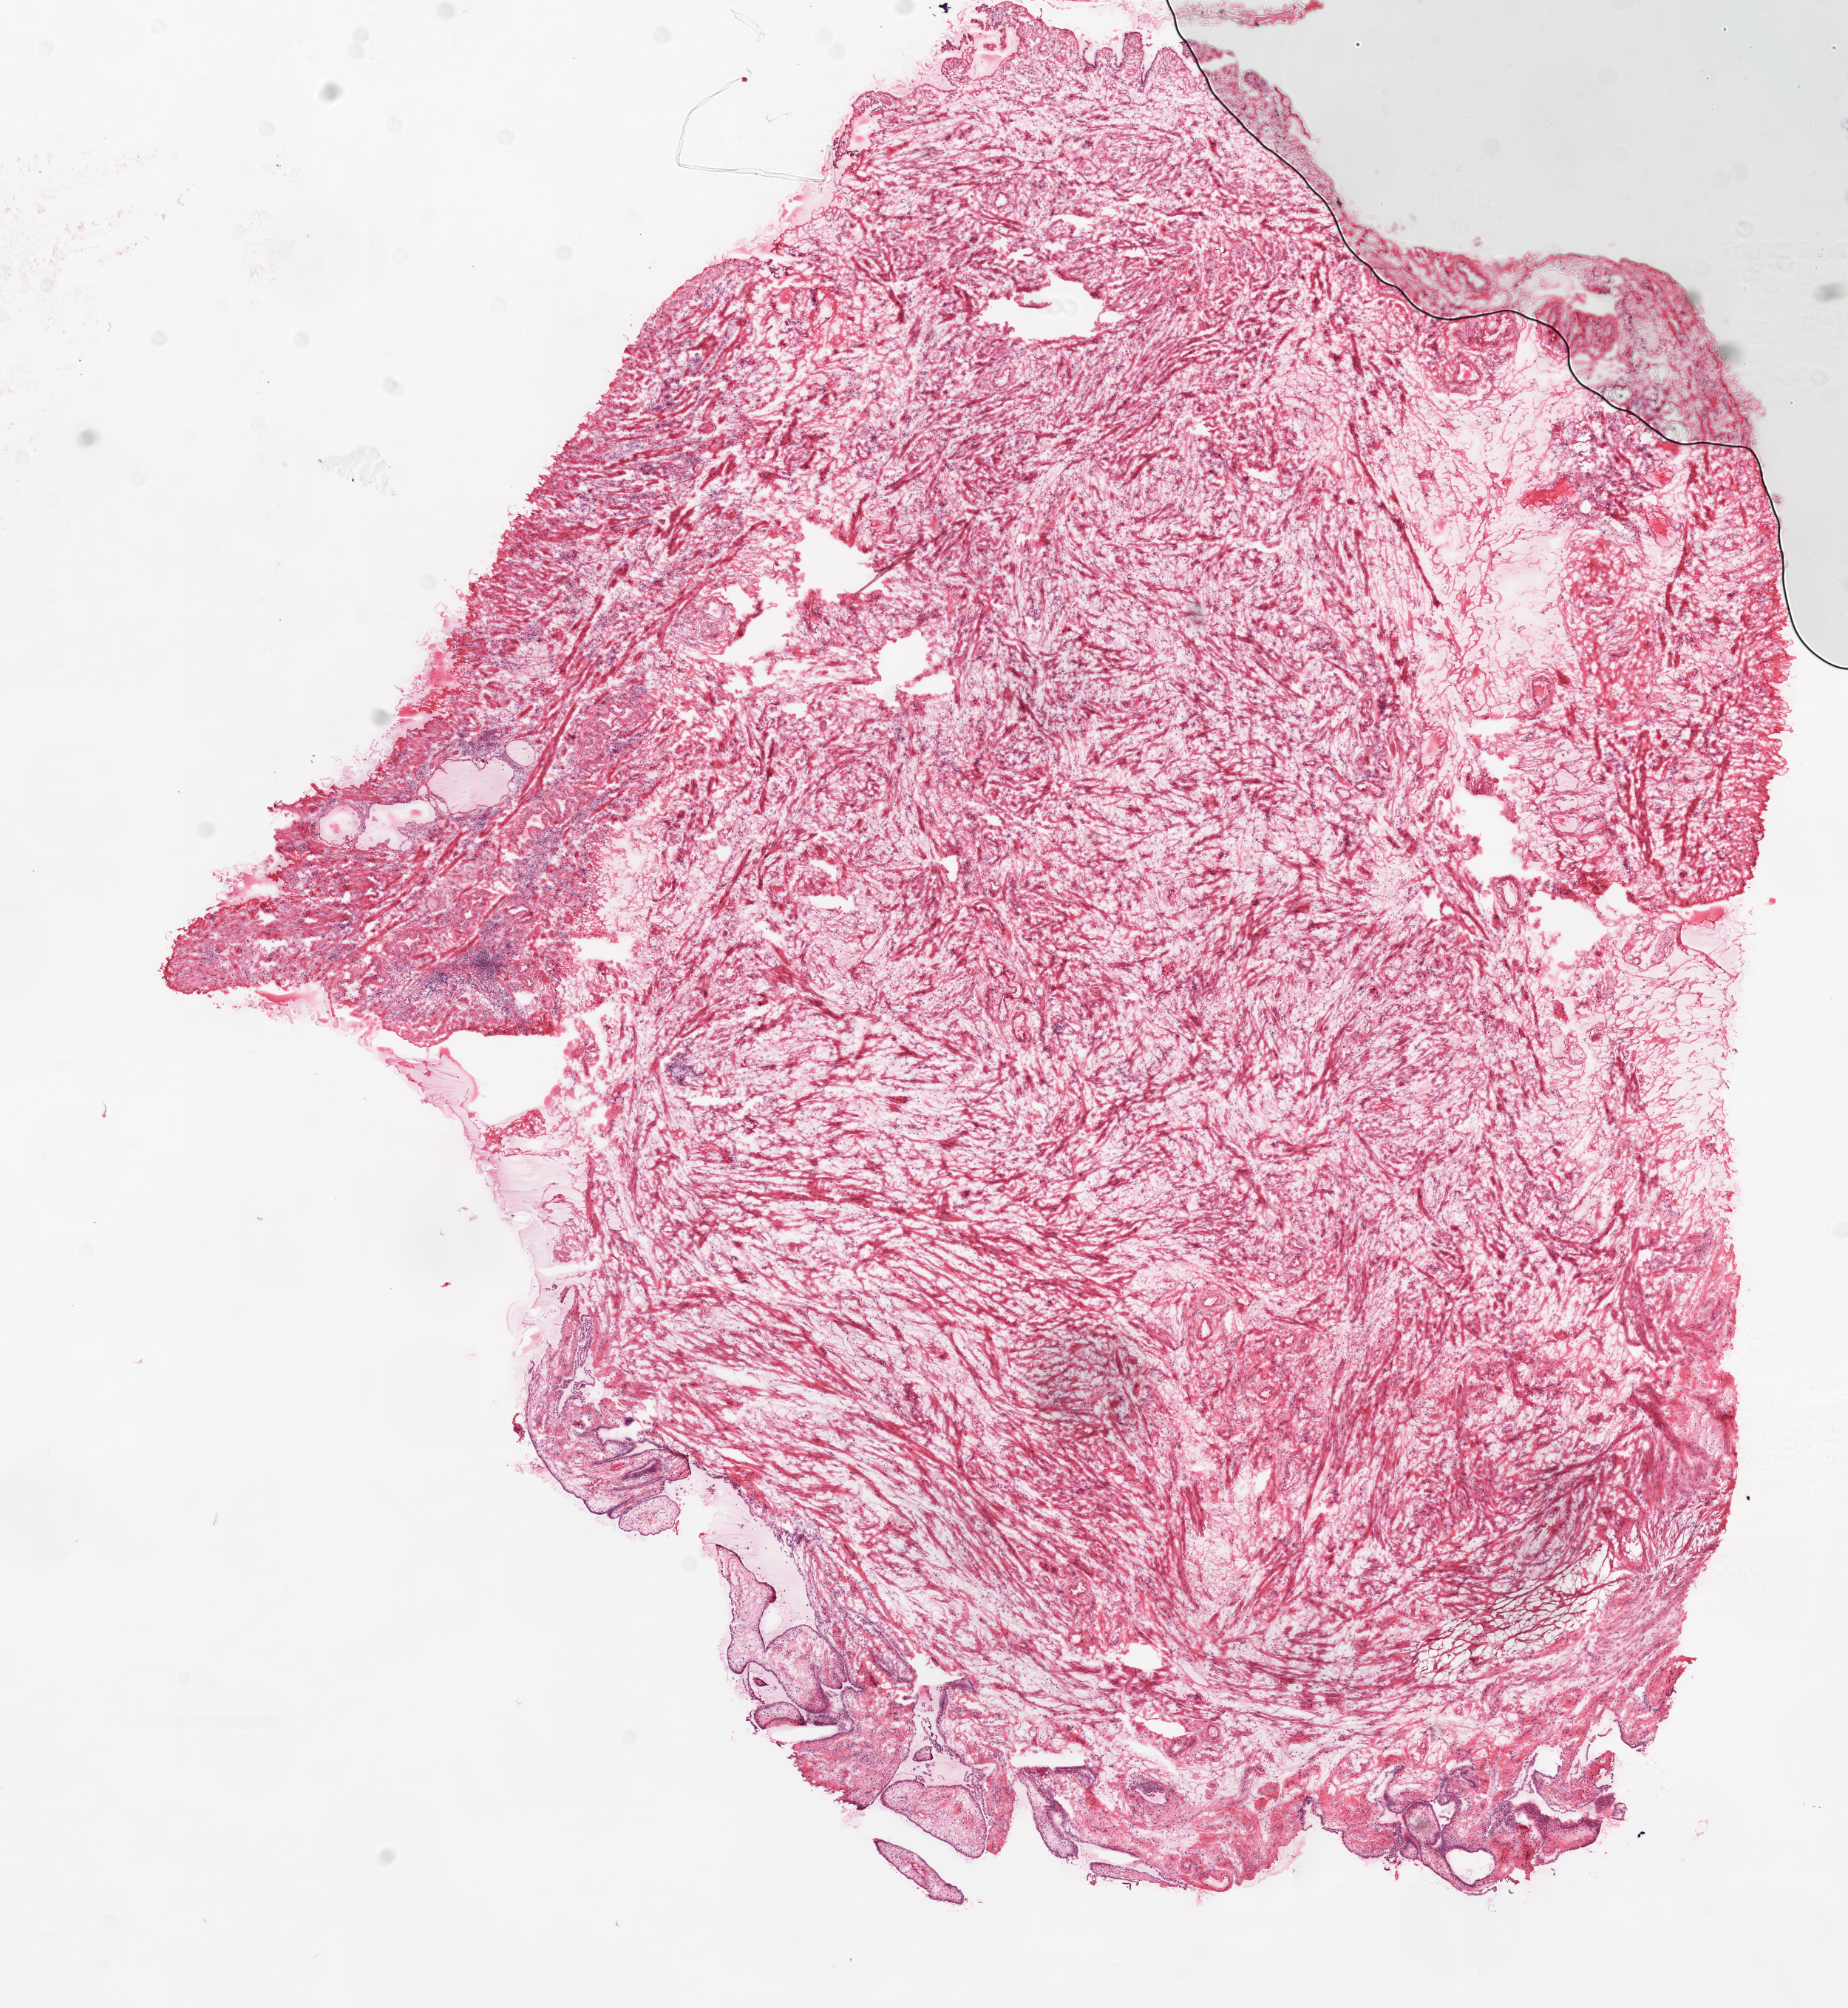
Whole-slide histology image, Hematoxylin and eosin (H&E) stained — shown as a low-resolution overview of the whole scanned area (about 10.0 x 10.9 mm, from a 20x scan), frozen section from the top of the tissue portion, sample: solid tissue normal (non-tumour tissue), ovary. Patient: female, age at initial diagnosis 55 years.
This section: solid tissue normal sample (biorepository sample class). Patient diagnosis: Serous cystadenocarcinoma, NOS.